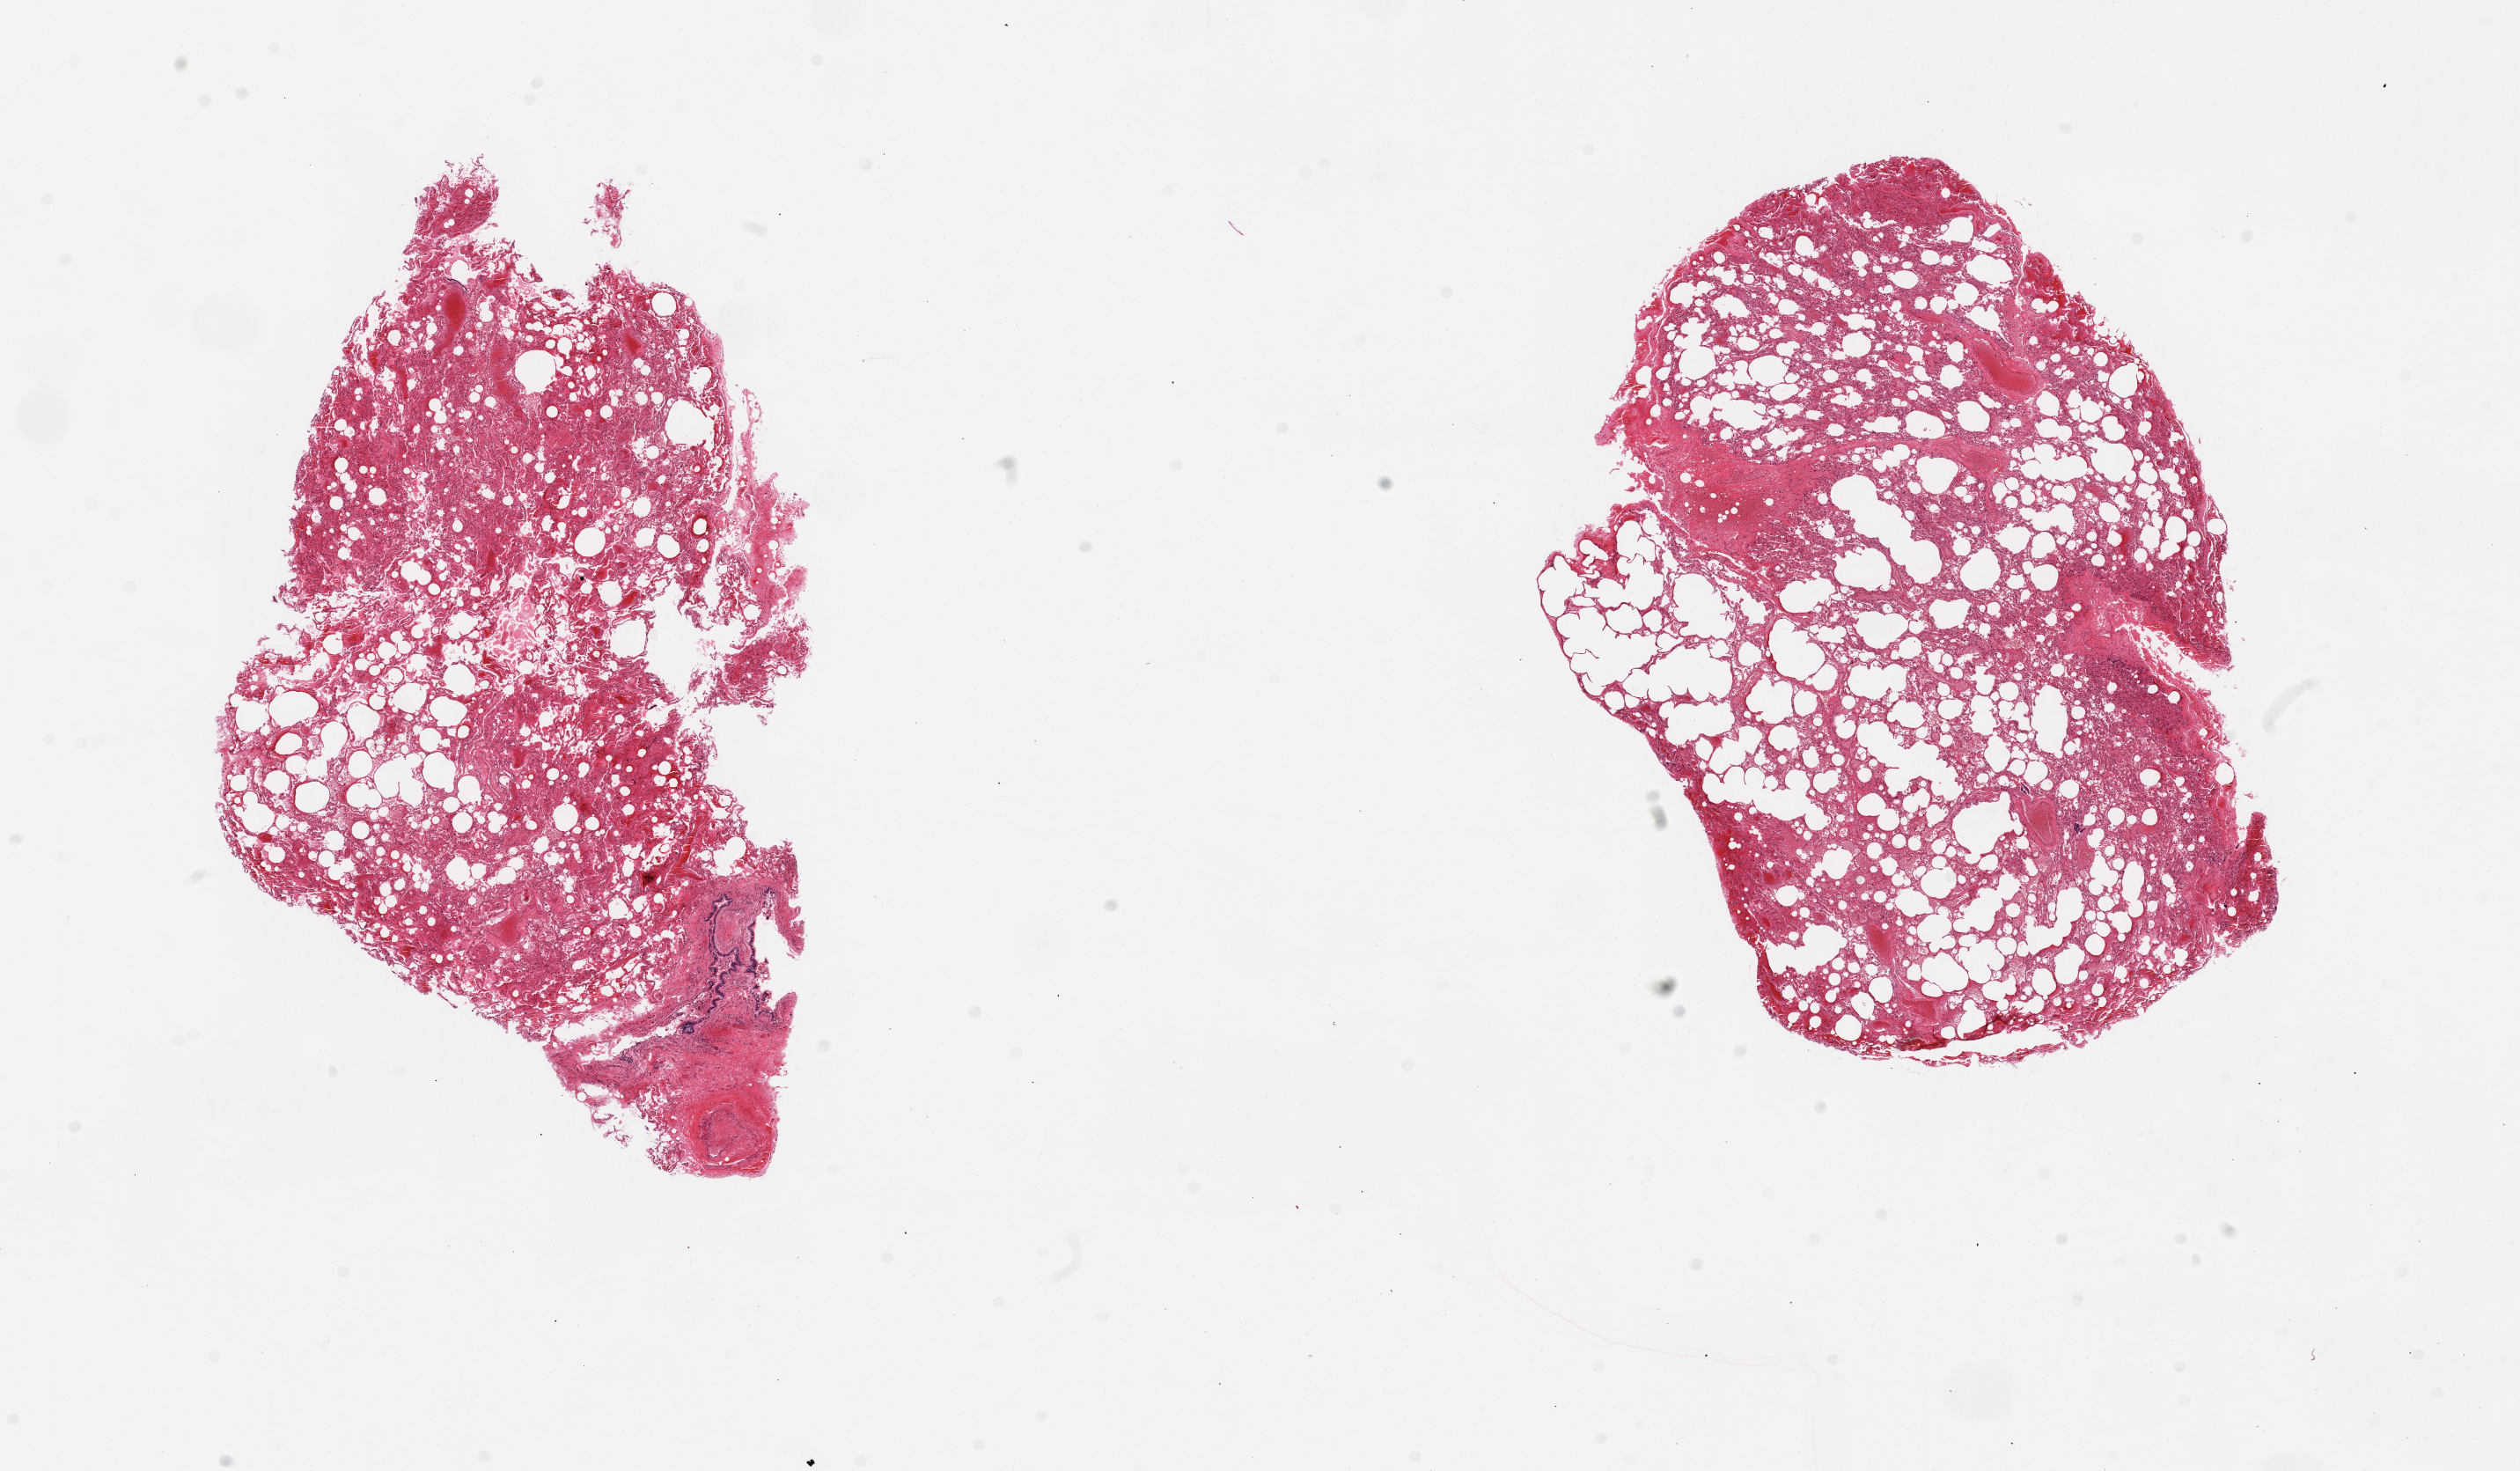
Whole-slide image, haematoxylin and eosin stain, a low-resolution overview of the entire scanned area, about 22.6 x 13.2 mm; PAXgene-fixed paraffin-embedded (PFPE) section; section of lung (target tissue); donor tissue sample. Male donor.
Reviewer comment on this tissue sample: 2 pieces, alveolar hemorrhage, edema, emphysematous change.